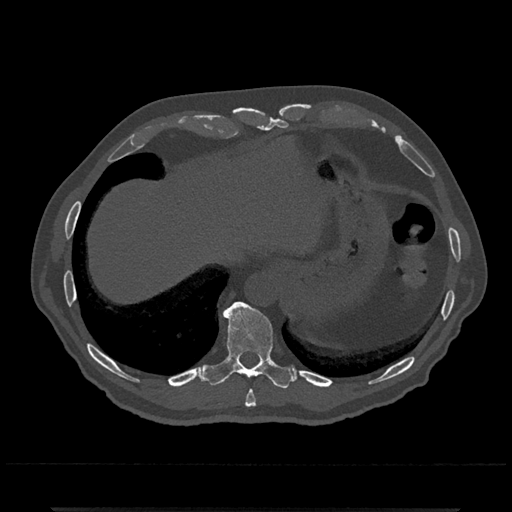
CT including the spine, one axial slice. Position 562 of 797 along the scan axis. Reconstruction kernel Br40s/3. Bone window (W 1800 / L 400 HU). 0.5 mm slice thickness. 512 × 512 image matrix, field of view 393 × 393 mm. Patient: male, 67 years. From the clinical record (not read from this slice): primary cancer: prostate.
Outlined on this slice (semi-automatically segmented with operator editing):
- T10 vertebra: bounding box [x1, y1, x2, y2] px = [203, 301, 293, 389]
- T9 vertebra: [245, 390, 256, 407]